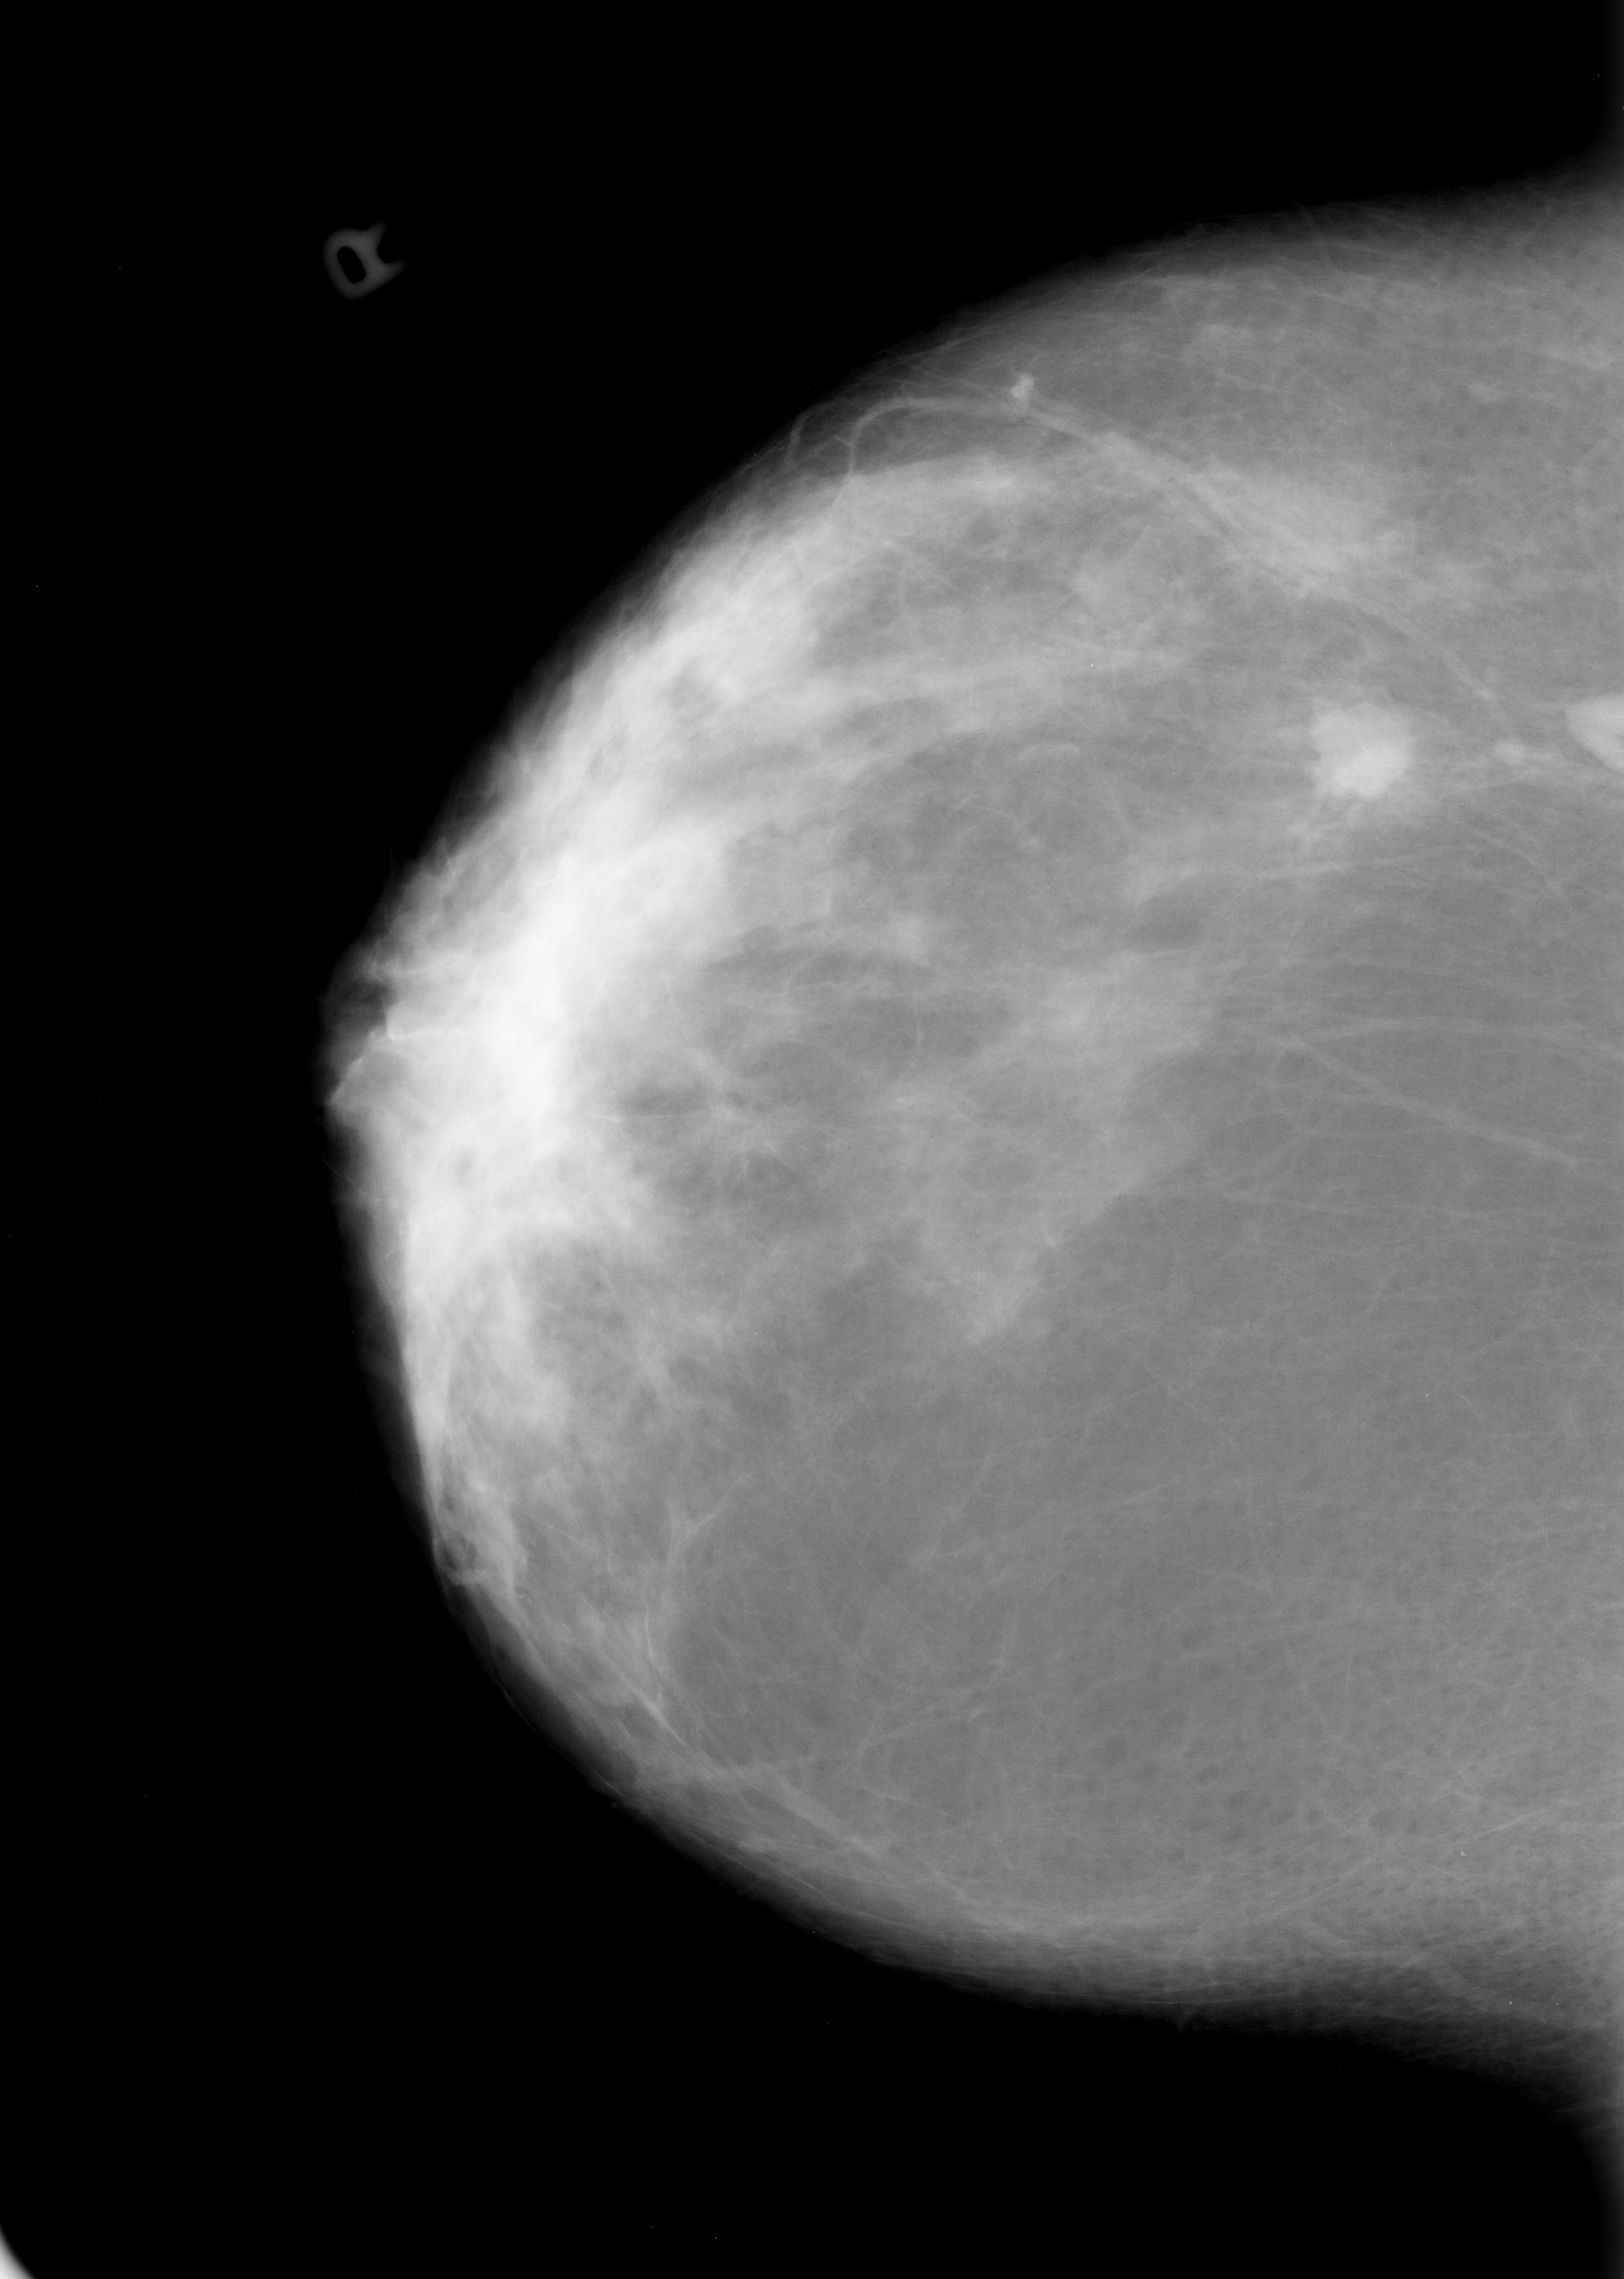
Mammogram (digitized film); right breast; craniocaudal (CC) view; BI-RADS breast density category 2 (scale 1–4); 1624 × 2279 image matrix.
Marked abnormalities (boxes around the expert regions of interest):
- mass, shape lobulated, margins circumscribed / ill defined; BI-RADS assessment category 4; pathology (as recorded): malignant: bounding box (x1, y1, x2, y2) in pixels: (1312, 706, 1417, 806)